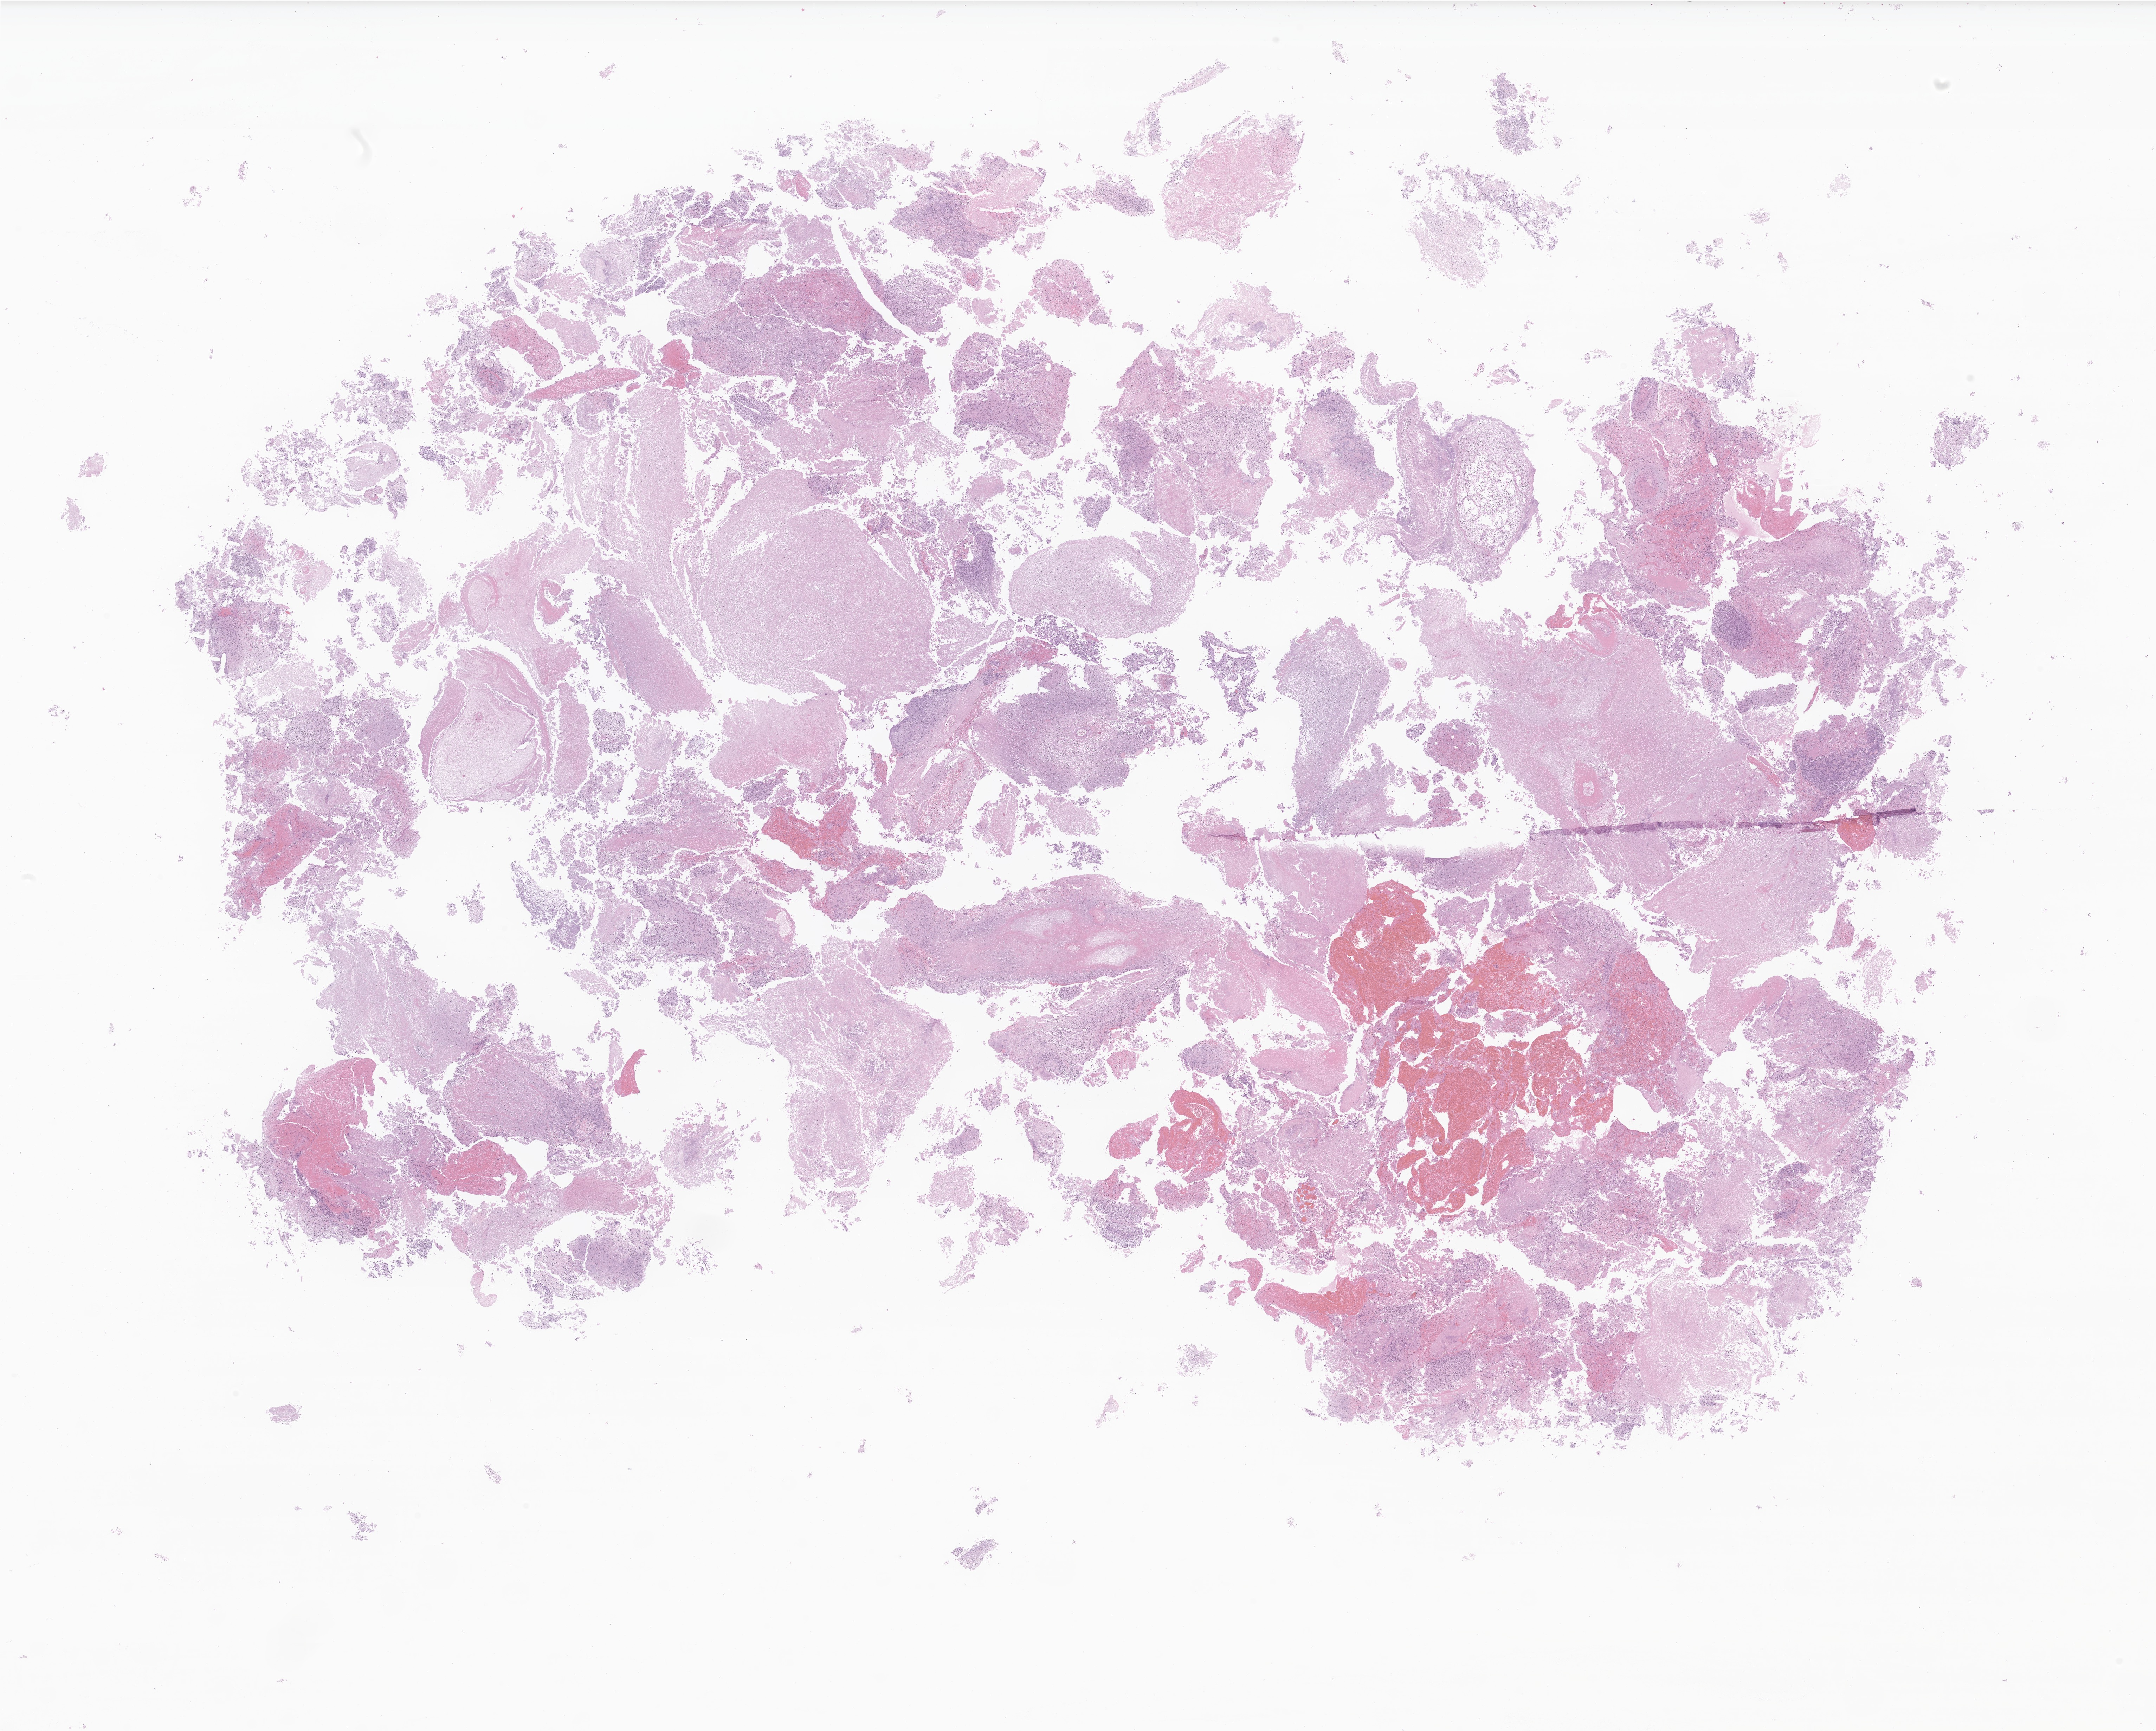
Haematoxylin and eosin whole-slide image of tumor tissue from the endometrium, low-resolution overview of the scanned area, about 25.9 x 20.8 mm, formalin-fixed, paraffin-embedded (FFPE) tissue. Female patient, age 194 months (16 years 2 months).
Recorded diagnosis: Carcinoma, metastatic, NOS.